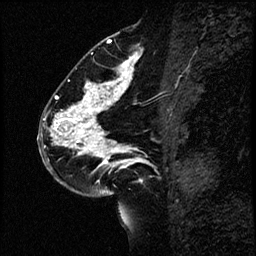
Breast MRI (dynamic contrast-enhanced), one sagittal slice; position 34 of 60 along the scan axis; dynamic contrast-enhanced study with each time point stored as its own series, time point 2 of 4 at this slice position (early post-contrast, ordered by acquisition time); 1.5 T; TE 4.2 ms, TR 17.6 ms; 256 × 256 image matrix, field of view 200 × 200 mm. Female patient, age 43 years. Case-level facts recorded for this patient, not image findings: setting: breast cancer imaged before/during neoadjuvant chemotherapy.
Structures marked on this image (semi-automatic segmentation, software-assisted and operator-edited):
- analysis volume of interest (the breast-tissue region the enhancement analysis was run in; not a lesion): bounding box <40,56,159,191> (left, top, right, bottom; pixels)
- tumour enhancement mask (voxels above the 100 % enhancement threshold inside the analysis volume of interest): <56,57,148,166>